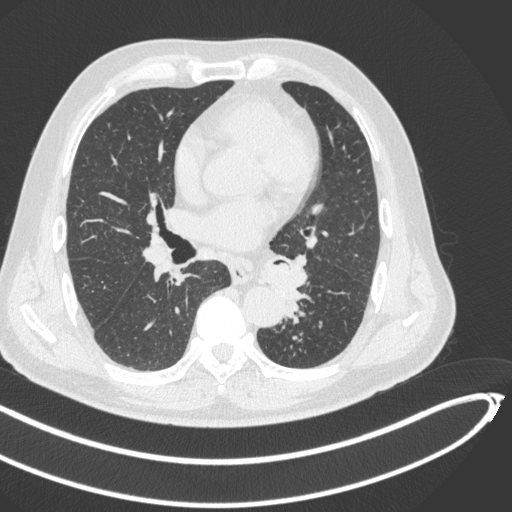
Chest CT, one axial slice. Slice 241 of 466 in the series (ordered by position). 120 kVp. Lung window (W 1500 / L -600 HU). 1 mm slice thickness. 512 × 512 image matrix. Patient: male, 64 years. From the clinical record (not read from this slice): clinical TNM (as recorded): T1c N0 M0; histopathological grade: G2.
Annotated regions visible in this slice (bounding box drawn by a radiologist):
- lung tumour (recorded histology: squamous cell carcinoma): box from (x=262, y=261) to (x=303, y=309) px